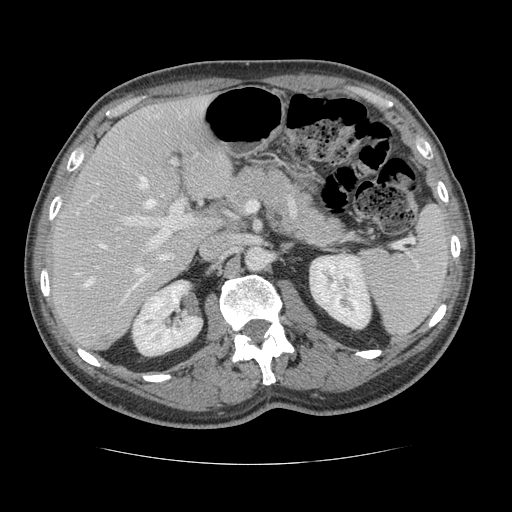
Contrast-enhanced abdominal CT, one axial slice; position 77 of 134 along the scan axis; soft-tissue window (W 400 / L 40 HU); 512 × 512 image matrix. Male patient, age 68 years. Case-level facts recorded for this patient, not image findings: diagnosis: colorectal cancer liver metastases, imaged before liver resection; multiple liver metastases: yes; largest metastasis: 2.2 cm; disease in both lobes: no.
Annotated regions visible in this slice (manually delineated by an expert):
- hepatic veins: bounding box [x1, y1, x2, y2] px = [76, 176, 155, 286]
- liver: [50, 97, 232, 350]
- planned liver remnant (the part of the liver to remain after resection): [50, 98, 232, 338]
- portal vein (with intrahepatic branches): [124, 160, 193, 299]
- liver metastasis: [96, 340, 110, 349]